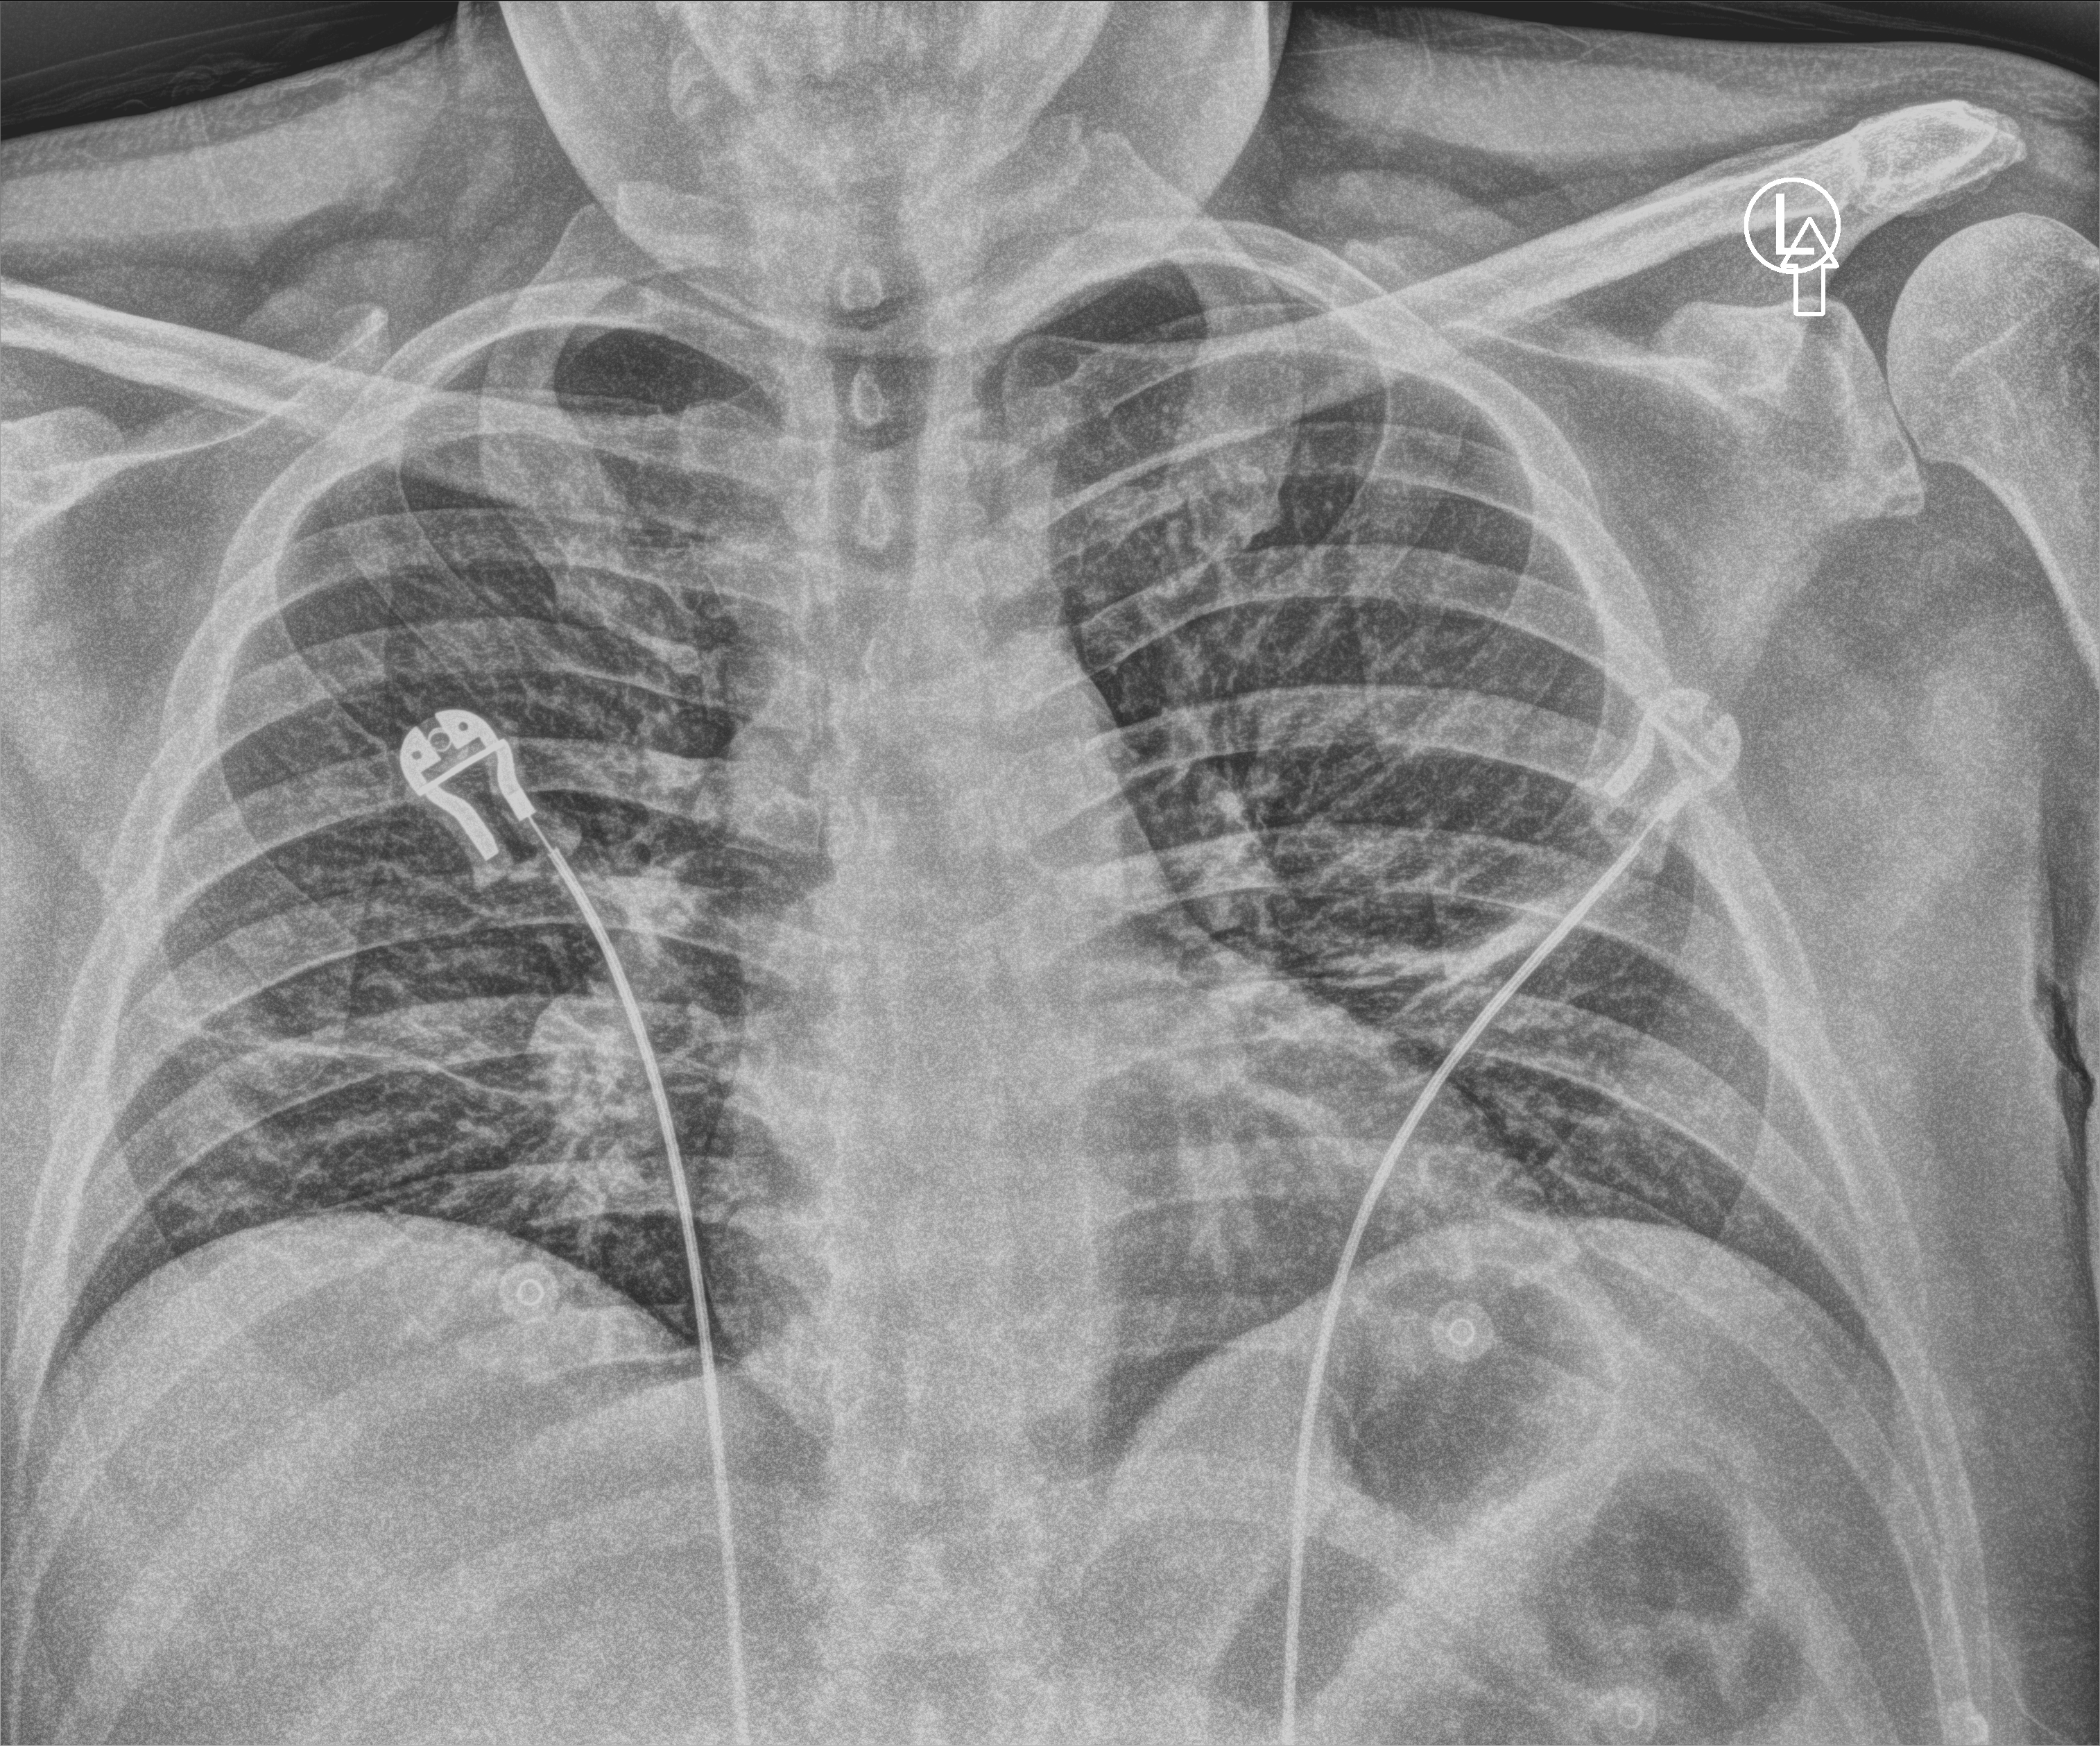
Portable chest radiograph. Male patient hospitalised with COVID-19, age 18–59 years.
Admission-level facts for this patient (not findings on this image; timing relative to this image not recorded):
- mechanically ventilated during this hospital stay: no